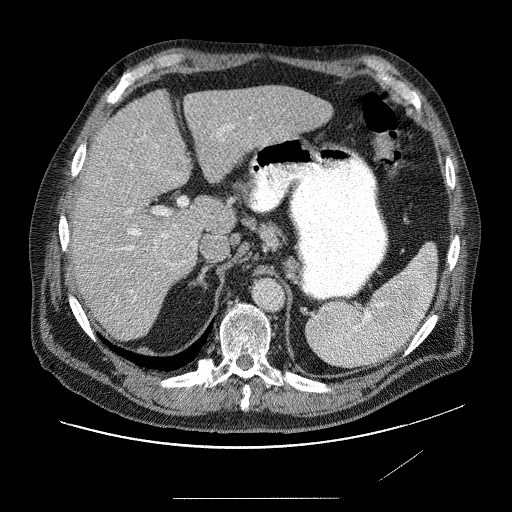
Contrast-enhanced abdominal CT (liver protocol), one axial slice; slice 50 of 89 in the series (ordered by position); reconstruction kernel STANDARD; 120 kVp; soft-tissue window (W 400 / L 40 HU); 512 × 512 image matrix, field of view 420 × 420 mm. From the clinical record (not read from this slice): diagnosis: hepatocellular carcinoma (patient treated with transarterial chemoembolisation; whether this scan precedes or follows treatment is not stated here); TNM stage (as recorded): Stage-IVA; Child-Pugh class: A; tumour nodularity: multinodular.
Structures marked on this image (semi-automatically segmented with operator editing):
- abdominal aorta: box from (x=253, y=279) to (x=283, y=310) px
- liver parenchyma outside the tumour (the mass and vessels are separate outlines, so this box may not span the whole liver): (x=66, y=84)–(x=336, y=333)
- mass: (x=149, y=143)–(x=189, y=260)
- liver vessels: (x=91, y=114)–(x=288, y=304)